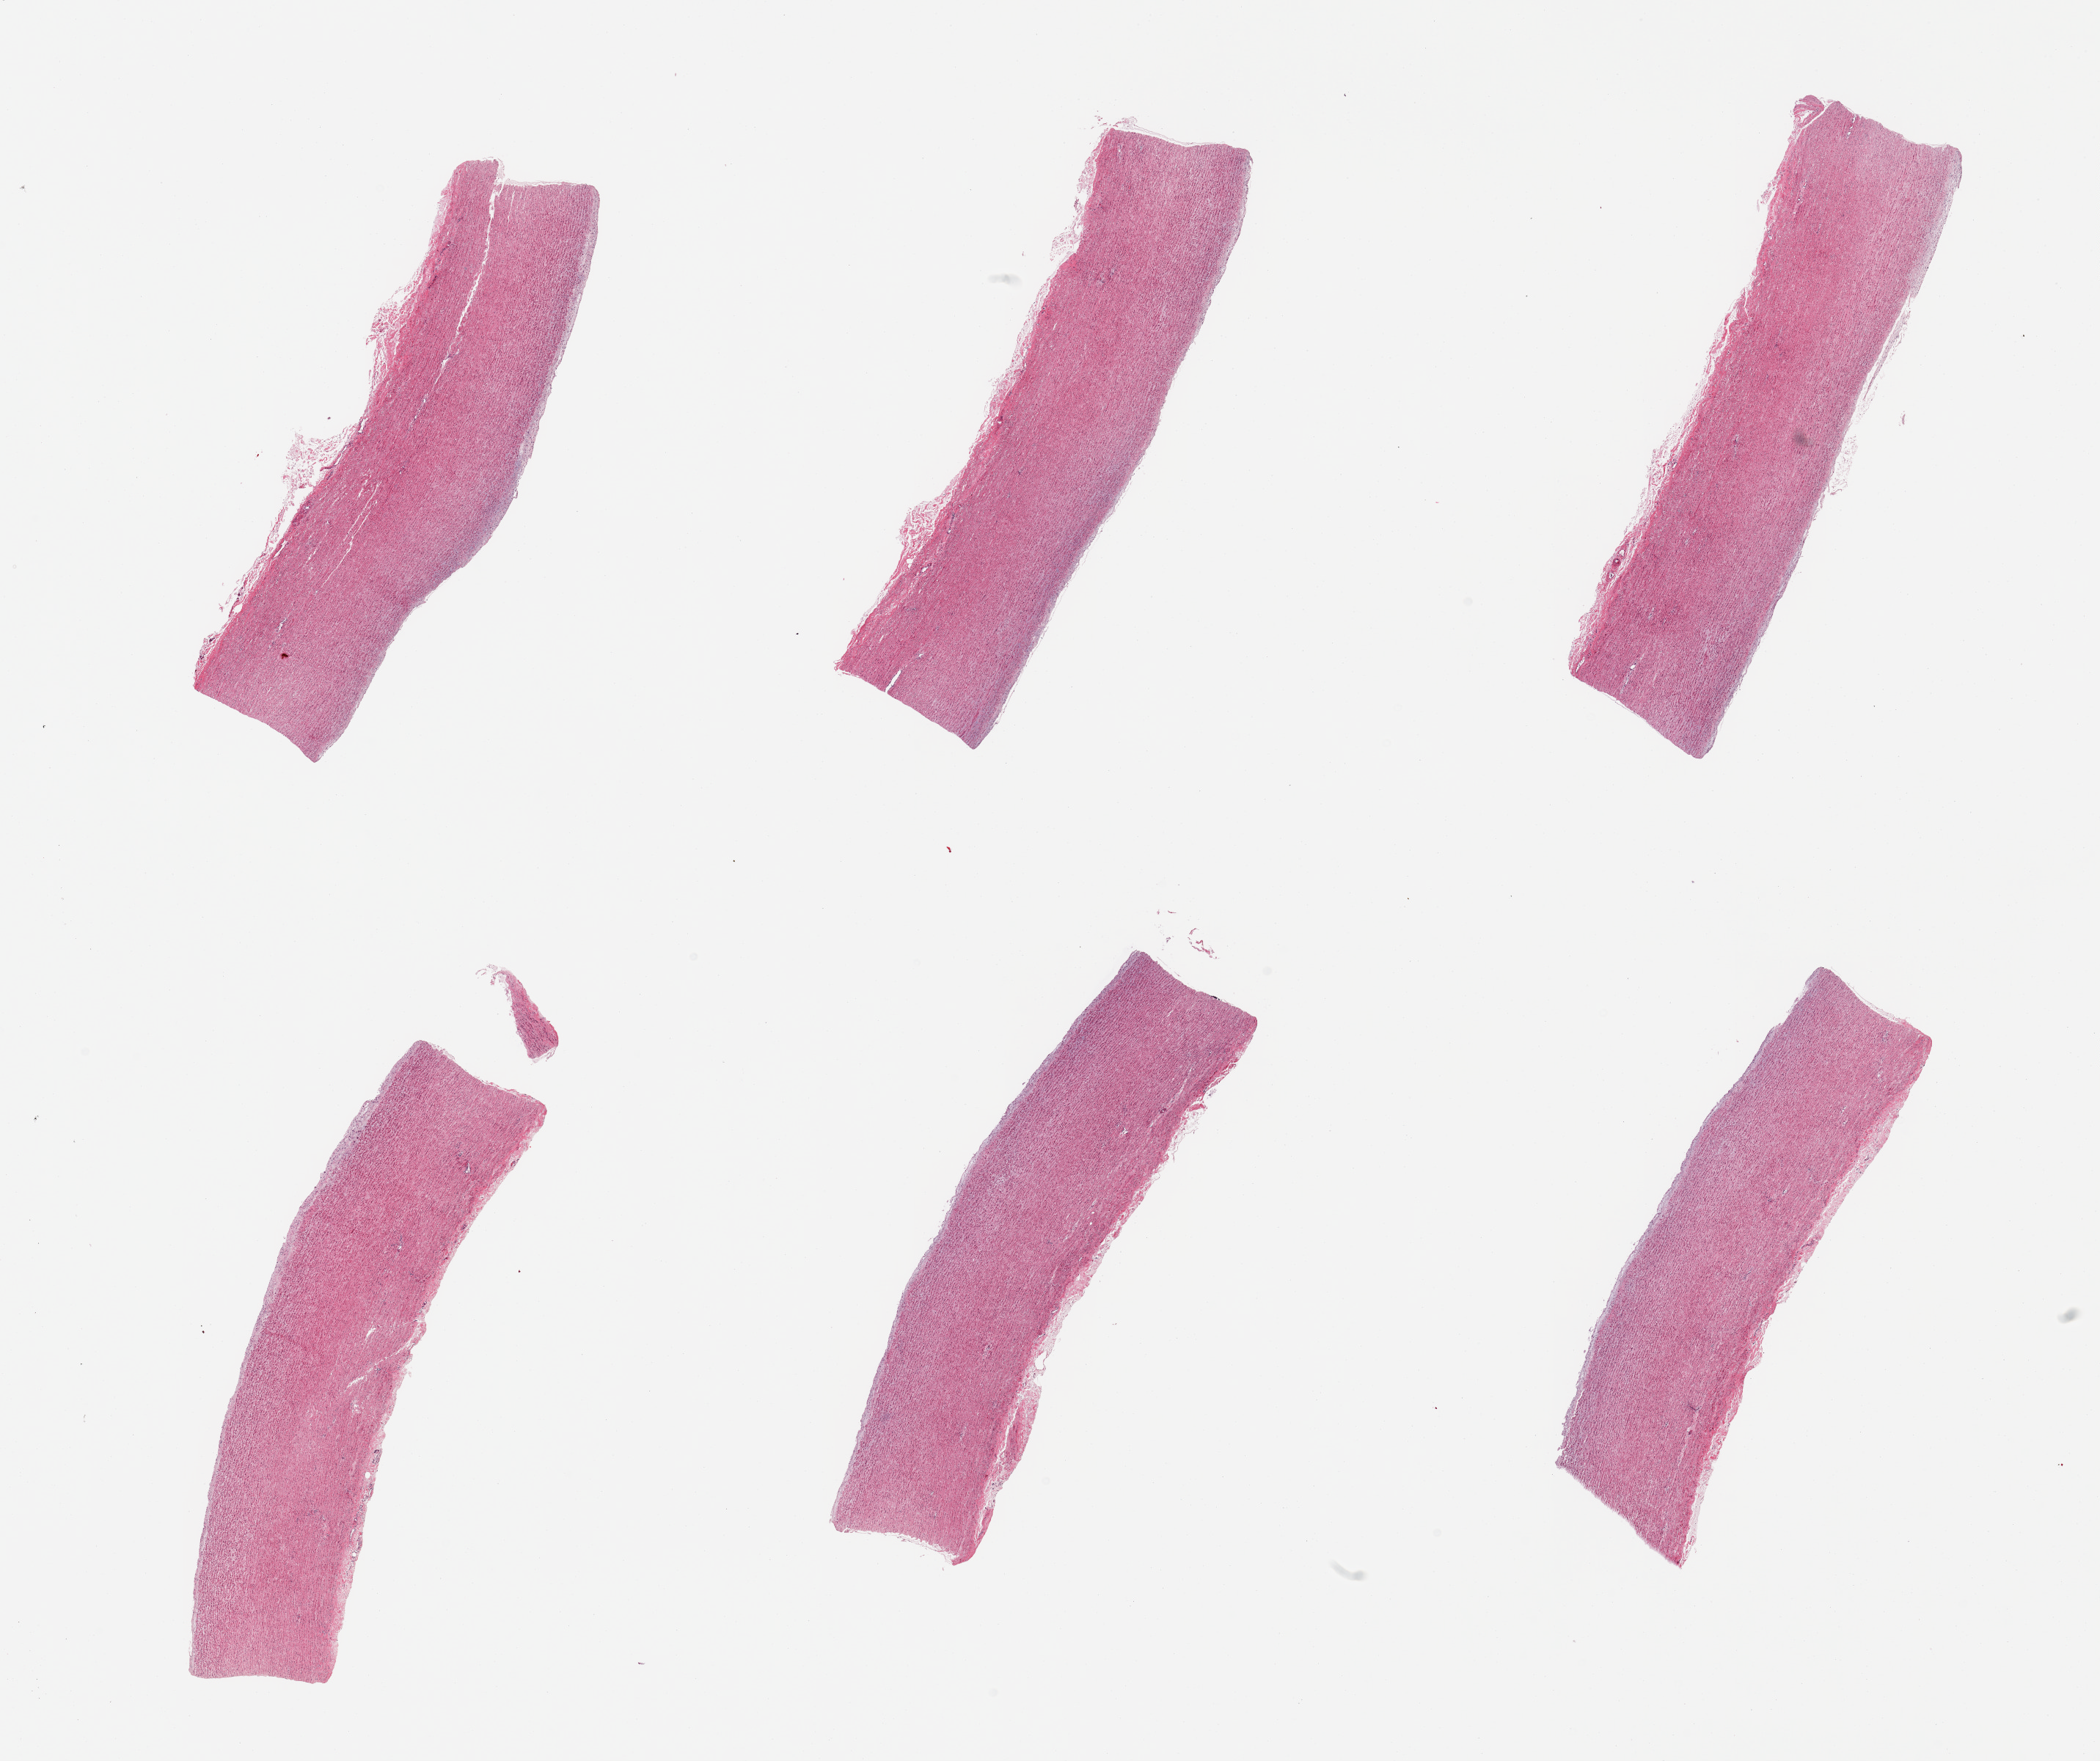
Hematoxylin and eosin (H&E) whole-slide image, whole scanned area (about 22.6 x 19.0 mm, from a 20x scan) shown as a low-resolution overview; PAXgene-fixed paraffin-embedded (PFPE) section; section of aorta (target tissue); donor tissue sample. Male donor.
- review note (as recorded): 6 pieces; mild atheromatous change